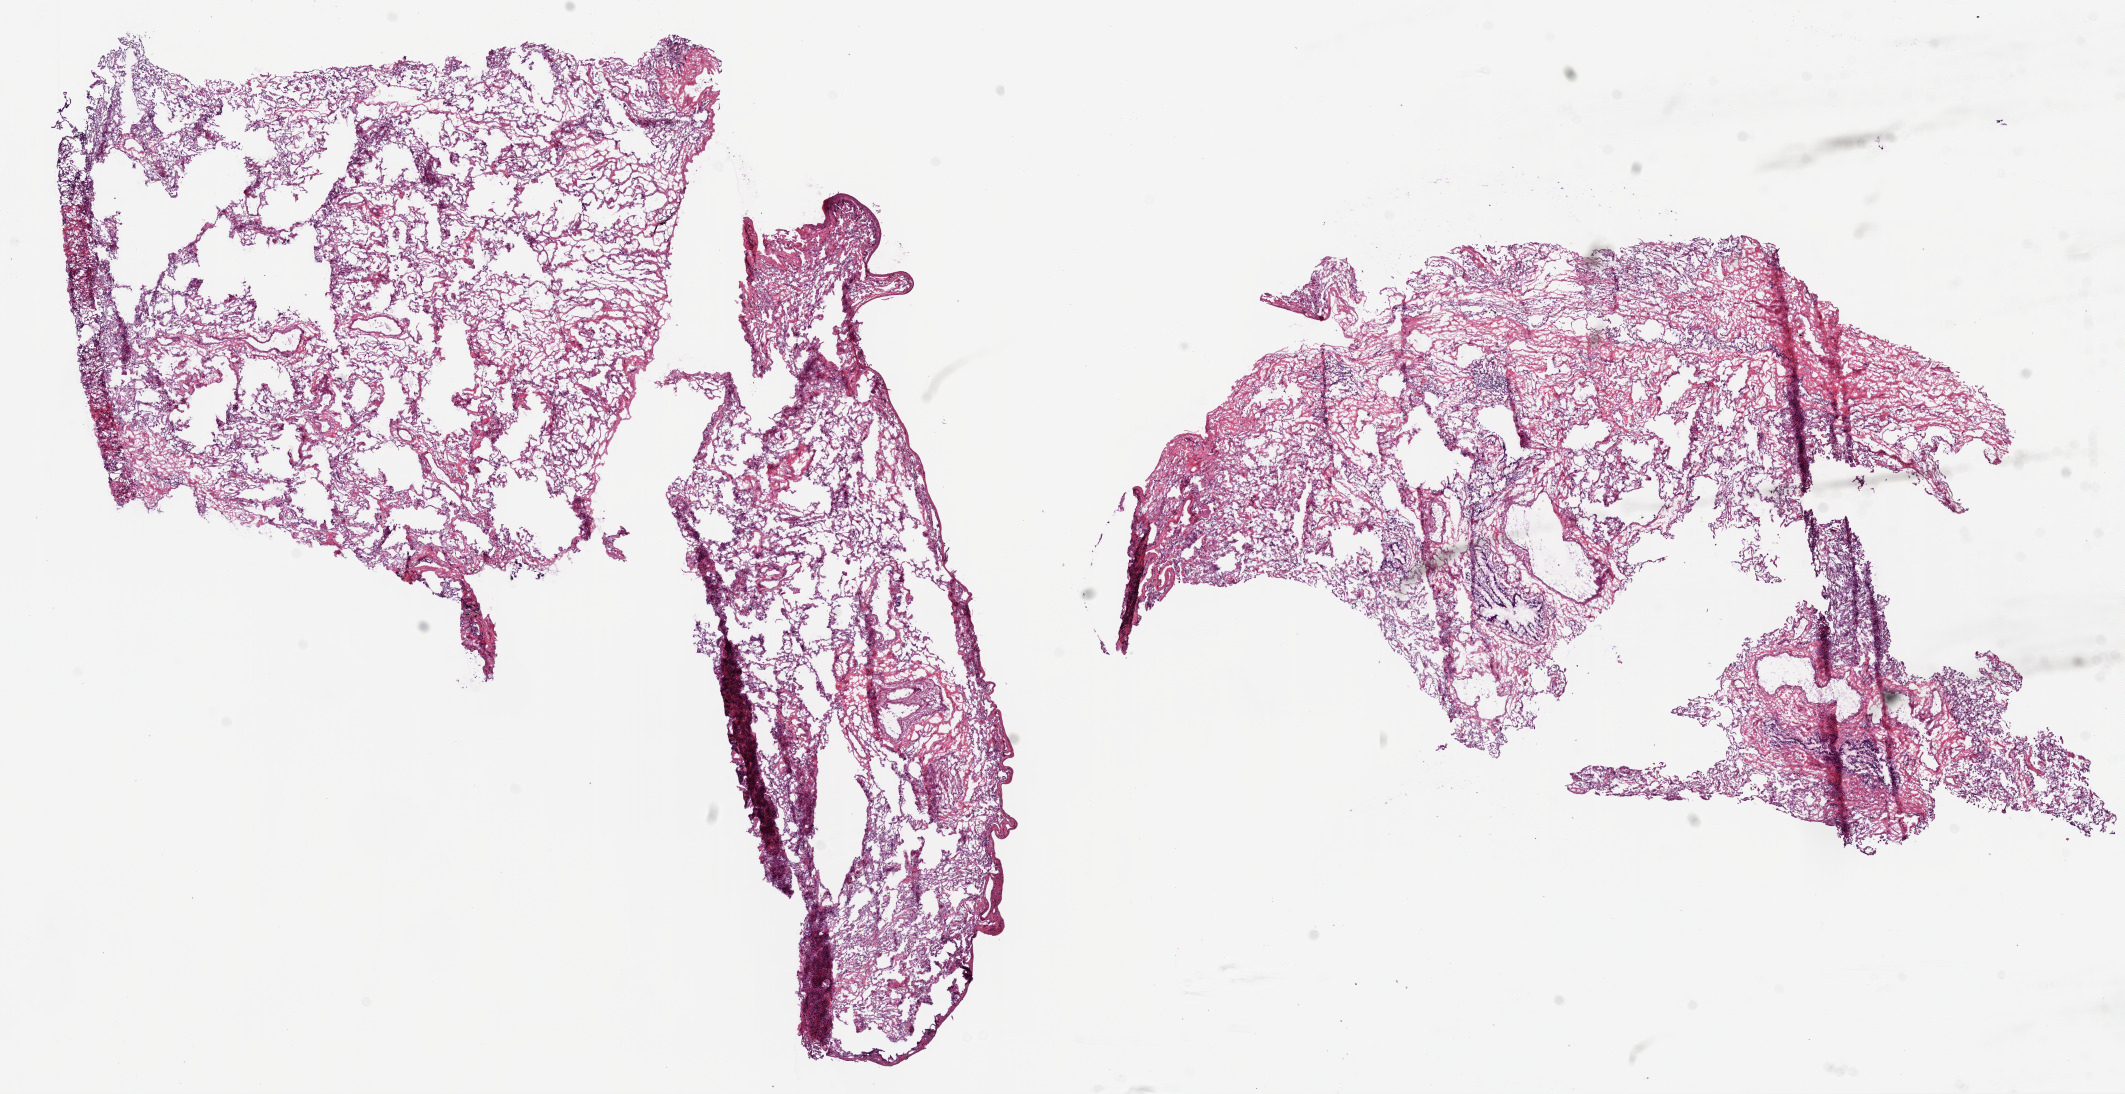
Hematoxylin and eosin (H&E) stained whole-slide image, a low-resolution overview of the entire scanned area, about 17.1 x 8.8 mm. Frozen section from the bottom of the tissue portion. Sample: solid tissue normal (non-tumour tissue), lung. Female, age 63 years at initial diagnosis.
This section: solid tissue normal sample (biorepository sample class). Patient diagnosis: Squamous cell carcinoma, small cell, nonkeratinizing (middle lobe, lung).